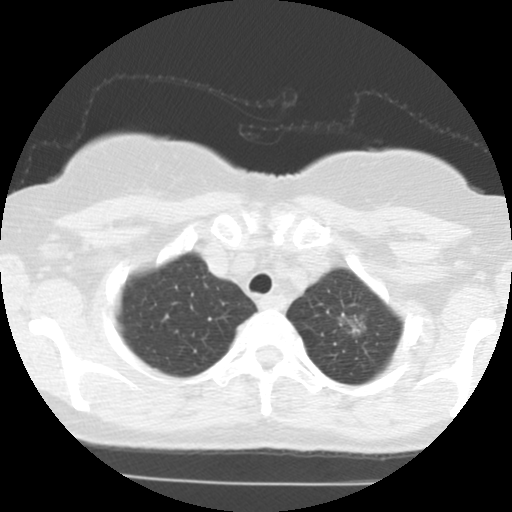
Low-dose screening chest CT, axial slice, baseline annual screen, lung window (W 1500 / L -600 HU), standard (soft-tissue) reconstruction kernel (STANDARD), 140 kVp, slice 103 of 123 in the series. Female, age 61 years at enrolment. Former smoker at enrolment.
Lesion marked by an expert reader, bounding box <324,303,377,352> (left, top, right, bottom; pixels). The screening reader recorded 2 non-calcified nodules or masses ≥4 mm on this exam (right lower lobe, left upper lobe); which of them this box marks is not recorded. Official screen result: positive, change unspecified: nodule(s) >= 4 mm or enlarging nodule(s), mass(es), or other non-specific abnormalities suspicious for lung cancer. Participant outcome: lung cancer diagnosed 79 days after this screen — adenocarcinoma, NOS, left upper lobe, stage IIIB (AJCC 6th edition), 15 mm at pathology.